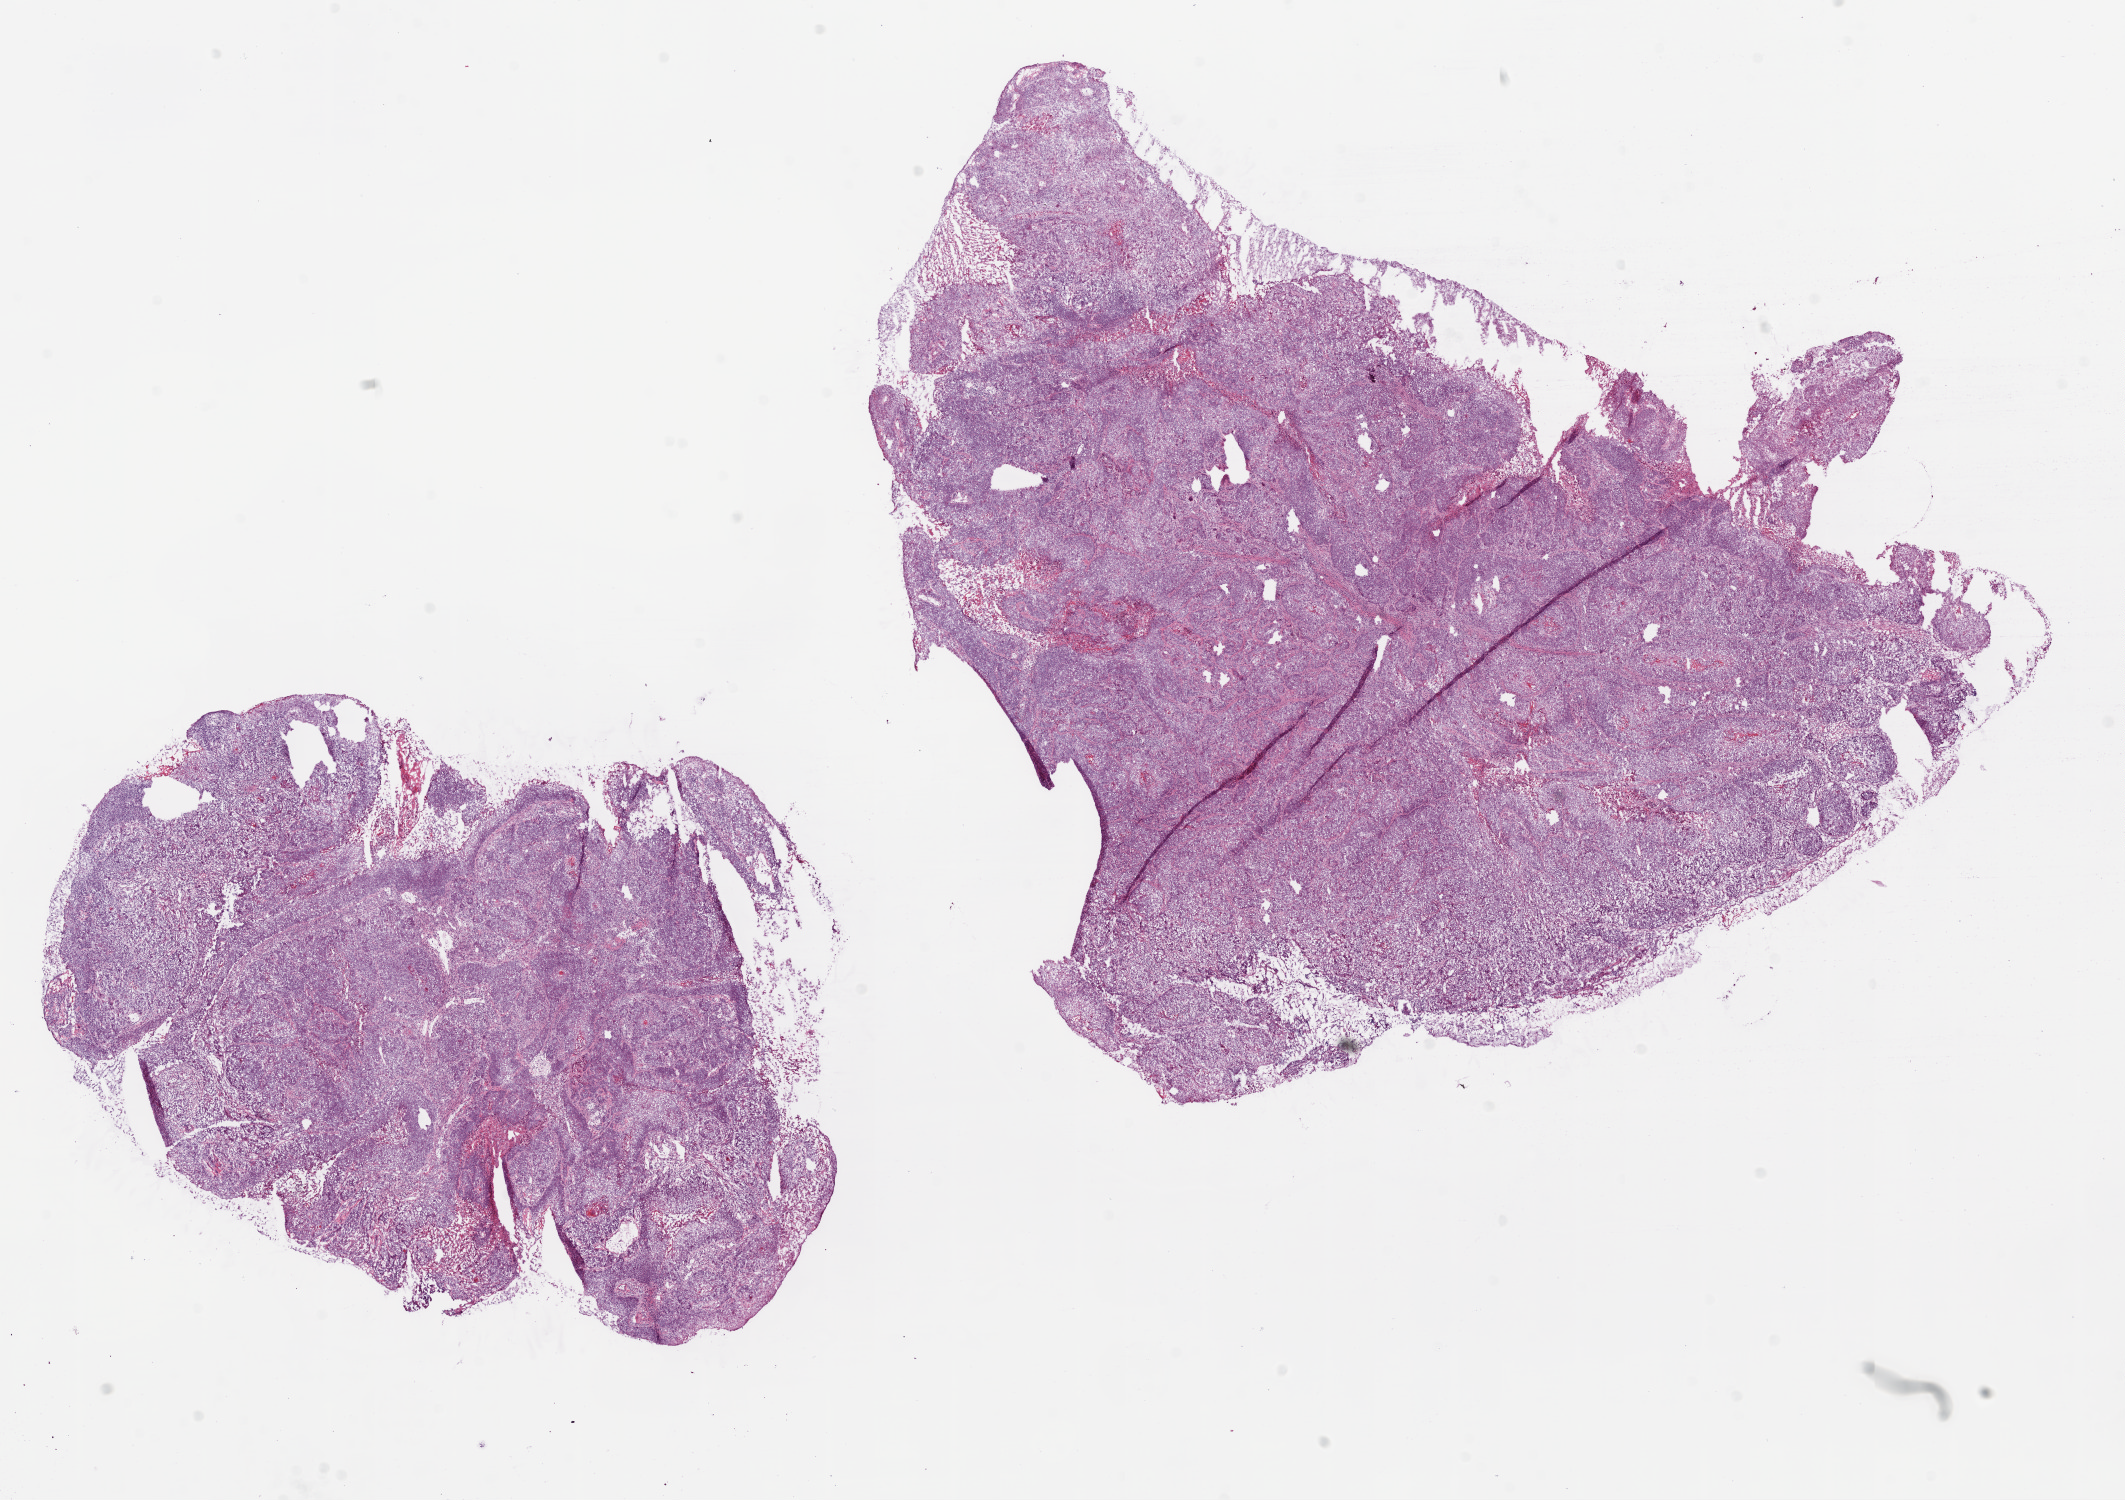
H&E whole-slide image, low-resolution overview of the scanned area, about 17.1 x 12.0 mm (slide scanned at 20x). Frozen section from the bottom of the tissue portion. Primary tumour sample from the lung. Male, age 65 years at initial diagnosis.
Pathologic diagnosis: Squamous cell carcinoma, NOS (upper lobe, lung).